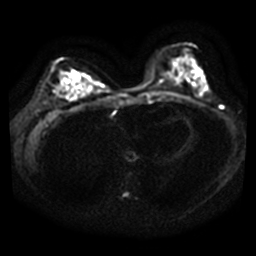
Breast MRI, one axial slice. Position 16 of 40 along the scan axis. Diffusion-weighted series; image 2 of 4 stored at this slice position (different b-values; order by instance number). 3 T. 5 mm slice thickness. 256 × 256 image matrix, field of view 340 × 340 mm. Female patient.
Structures marked on this image (manually delineated by an expert):
- tumour on diffusion-weighted imaging: bounding box (x1, y1, x2, y2) in pixels: (77, 72, 81, 79)